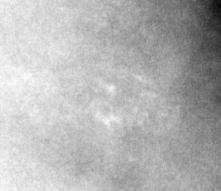
Region of interest cut from a scanned film mammogram (one marked finding), right breast, MLO view, BI-RADS breast density category 4 (scale 1–4).
Marked abnormality: calcifications, morphology pleomorphic, distribution clustered; BI-RADS assessment category 4; subtlety rating 2 on a 1 (subtle) to 5 (obvious) scale; pathology (as recorded): malignant.